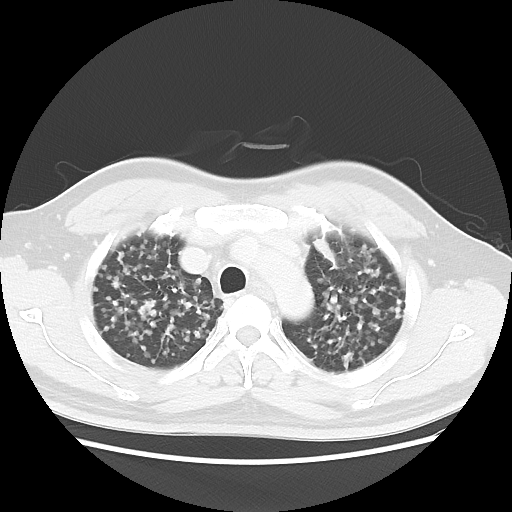
Chest CT, one axial slice; slice 31 of 40 in the series (ordered by position); reconstruction kernel LUNG; lung window (W 1500 / L -600 HU); 5 mm slice thickness; 512 × 512 image matrix, field of view 366 × 366 mm. Patient: male, 41 years. Case-level facts recorded for this patient, not image findings: clinical TNM (as recorded): T1c N3 M1b.
Outlined on this slice (rectangle marked by the reading radiologist):
- lung tumour (recorded histology: adenocarcinoma): bounding box [x1, y1, x2, y2] px = [310, 232, 336, 269]